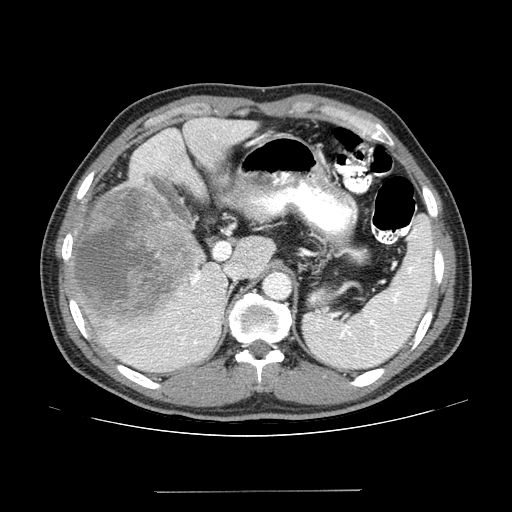
Contrast-enhanced abdominal CT (liver protocol), one axial slice. Position 92 of 131 along the scan axis. 100 kVp. One of 2 acquisitions stored at this slice position. Soft-tissue window (W 400 / L 40 HU). 2.5 mm slice thickness. 512 × 512 image matrix, field of view 380 × 380 mm. From the clinical record (not read from this slice): diagnosis: hepatocellular carcinoma (patient treated with transarterial chemoembolisation; whether this scan precedes or follows treatment is not stated here); TNM stage (as recorded): Stage-I; Child-Pugh class: A; tumour differentiation: poorly differentiated.
Outlined on this slice (semi-automatically segmented with operator editing):
- liver parenchyma outside the tumour (the mass and vessels are separate outlines, so this box may not span the whole liver): bounding box <66,117,258,372> (left, top, right, bottom; pixels)
- mass: <69,183,203,324>
- liver vessels: <129,128,247,364>